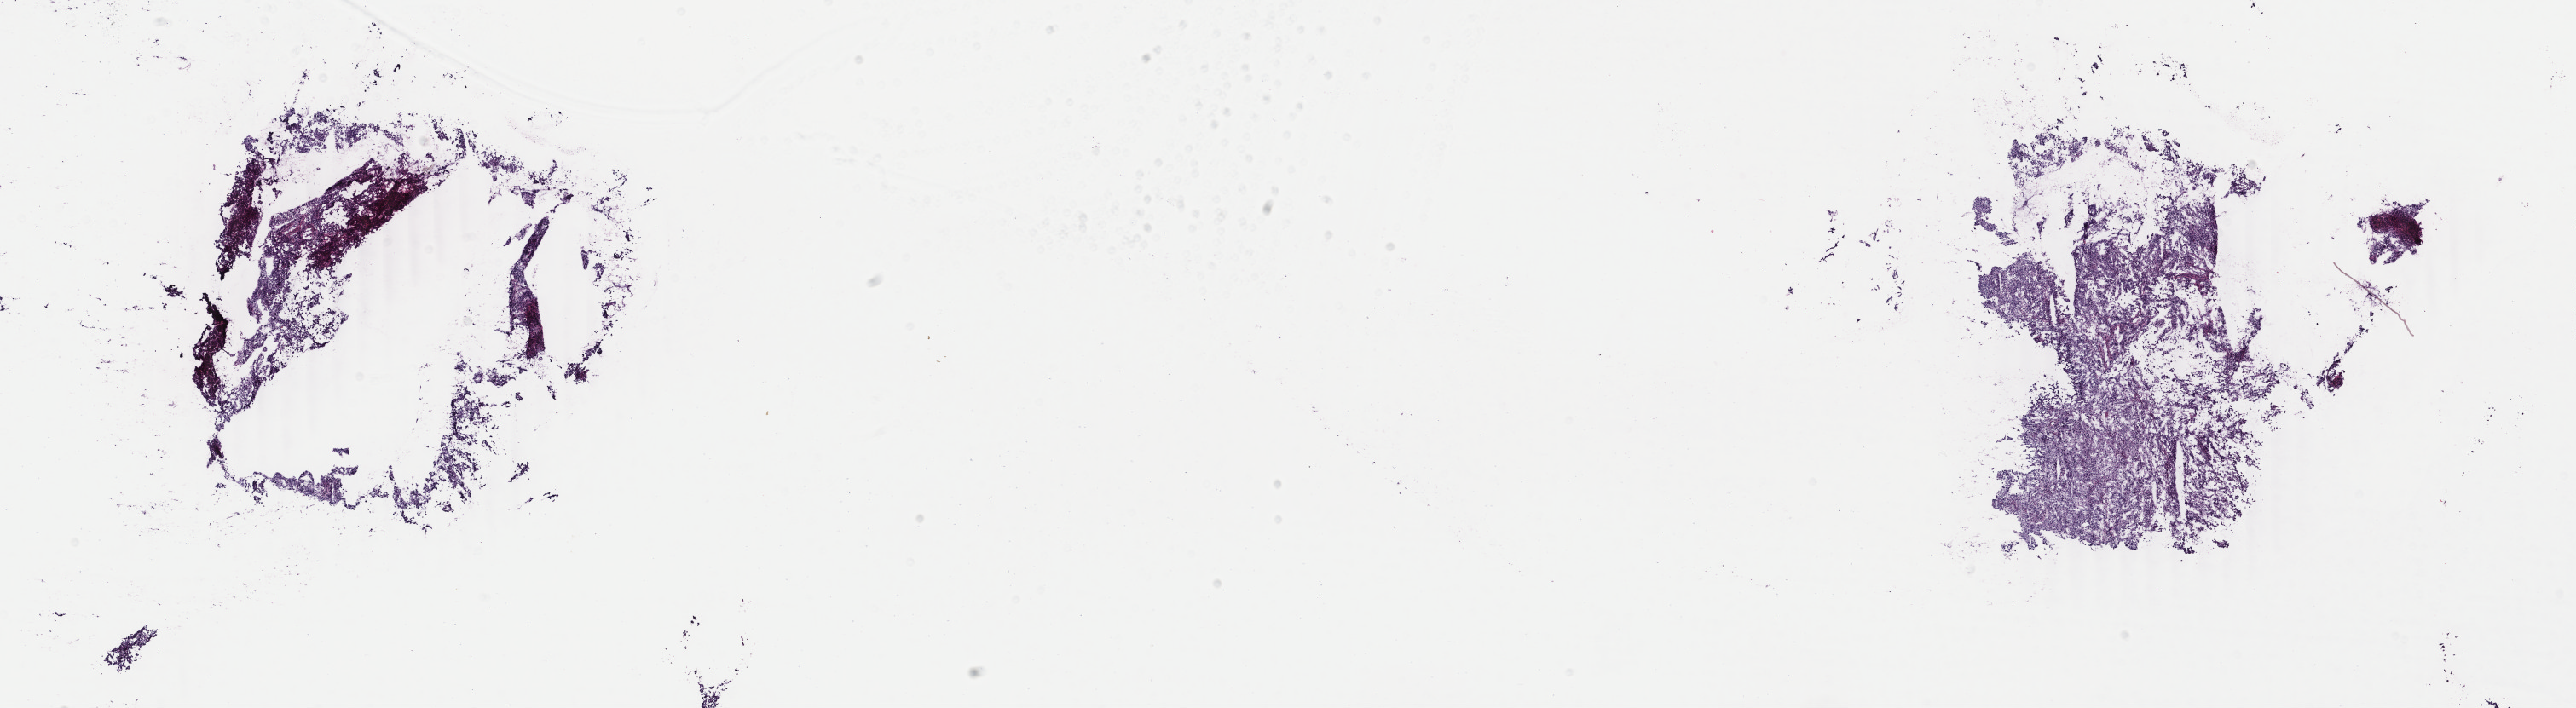
Hematoxylin and eosin (H&E) stained whole-slide image — whole scanned area (about 24.0 x 6.6 mm) shown as a low-resolution overview, frozen section from the top of the tissue portion, uterus, primary tumour sample. Patient: female, age at initial diagnosis 64 years. Histologic grade: G3 (poorly differentiated). Composition of this section per pathologist review: tumour cells 100%, tumour nuclei 98%, normal cells 0%, stromal cells 0%, necrosis 0%. Inflammatory infiltration, as recorded: lymphocyte infiltration 0%, monocyte infiltration 0%, neutrophil infiltration 0%.
- histologic diagnosis: Endometrioid adenocarcinoma, NOS (endometrium)
- FIGO stage: IC